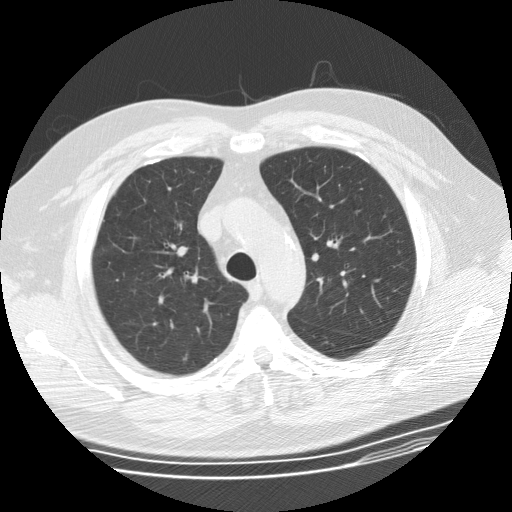
Low-dose screening chest CT, one axial slice. Position 114 of 155 along the scan axis. Lung window (W 1500 / L -600 HU). 2.5 mm slice thickness. 512 × 512 image matrix, field of view 380 × 380 mm.
Outlined on this slice (outlined manually by an expert reader):
- lesion 1 (tumor, upper lobe of right lung): bounding box <183,354,188,360> (left, top, right, bottom; pixels)